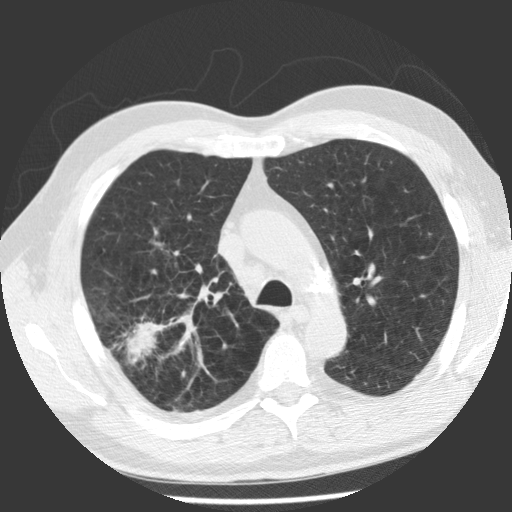
Low-dose screening chest CT, one axial slice; slice 78 of 112 in the series (ordered by position); reconstruction kernel STANDARD; 140 kVp; lung window (W 1500 / L -600 HU); 2.5 mm slice thickness; 512 × 512 image matrix, field of view 344 × 344 mm.
Annotated regions visible in this slice (manually delineated by an expert):
- lesion 1 (tumor, upper lobe of right lung): bounding box [x1, y1, x2, y2] px = [125, 322, 164, 357]